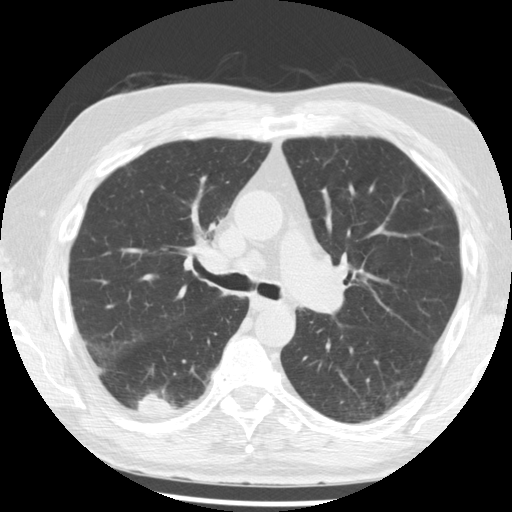
Low-dose screening chest CT, one axial slice; slice 131 of 221 in the series (ordered by position); reconstruction kernel STANDARD; lung window (W 1500 / L -600 HU); 512 × 512 image matrix, field of view 350 × 350 mm.
Outlined on this slice (manually delineated by an expert):
- lesion 1 (tumor, lower lobe of right lung): bounding box [x1, y1, x2, y2] px = [138, 390, 179, 414]